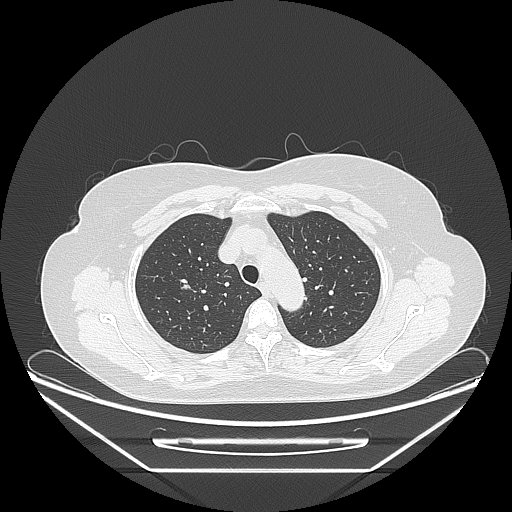
Chest CT, one axial slice; slice 191 of 236 in the series (ordered by position); reconstruction kernel LUNG; 120 kVp; lung window (W 1500 / L -600 HU); 1.25 mm slice thickness; 512 × 512 image matrix, field of view 433 × 433 mm. Female patient, age 60 years. Case-level facts recorded for this patient, not image findings: clinical TNM (as recorded): T1c N0 M0; histopathological grade: G2-3.
Annotated regions visible in this slice (bounding box drawn by a radiologist):
- lung tumour (recorded histology: adenocarcinoma): bounding box (x1, y1, x2, y2) in pixels: (175, 271, 199, 302)